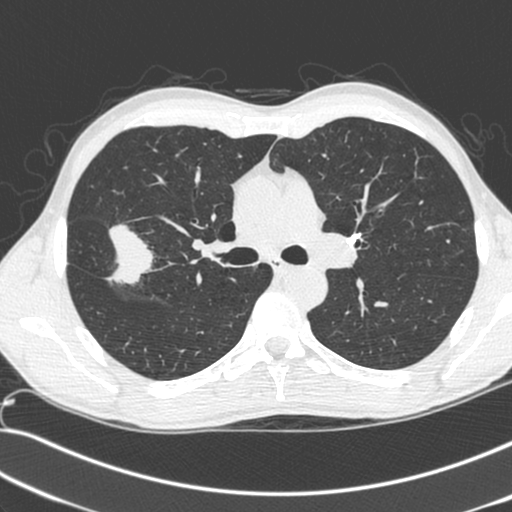
Chest CT (low-dose screening protocol), one axial image; baseline screening round; lung window (W 1500 / L -600 HU); 1.3 mm slice thickness; slice 93 of 281 in the series; 512 × 512 image matrix, field of view 341 × 341 mm. Male, age 55 years at enrolment. Current smoker at enrolment.
Expert reader's lesion annotation, bounding box [x1, y1, x2, y2] px = [67, 218, 157, 296]. Screening reader's record for this exam (one nodule recorded; not confirmed to be the boxed lesion): non-calcified nodule or mass ≥4 mm, right upper lobe, 52 × 39 mm, spiculated (stellate) margins, soft tissue attenuation. Official screen result: positive, change unspecified: nodule(s) >= 4 mm or enlarging nodule(s), mass(es), or other non-specific abnormalities suspicious for lung cancer.